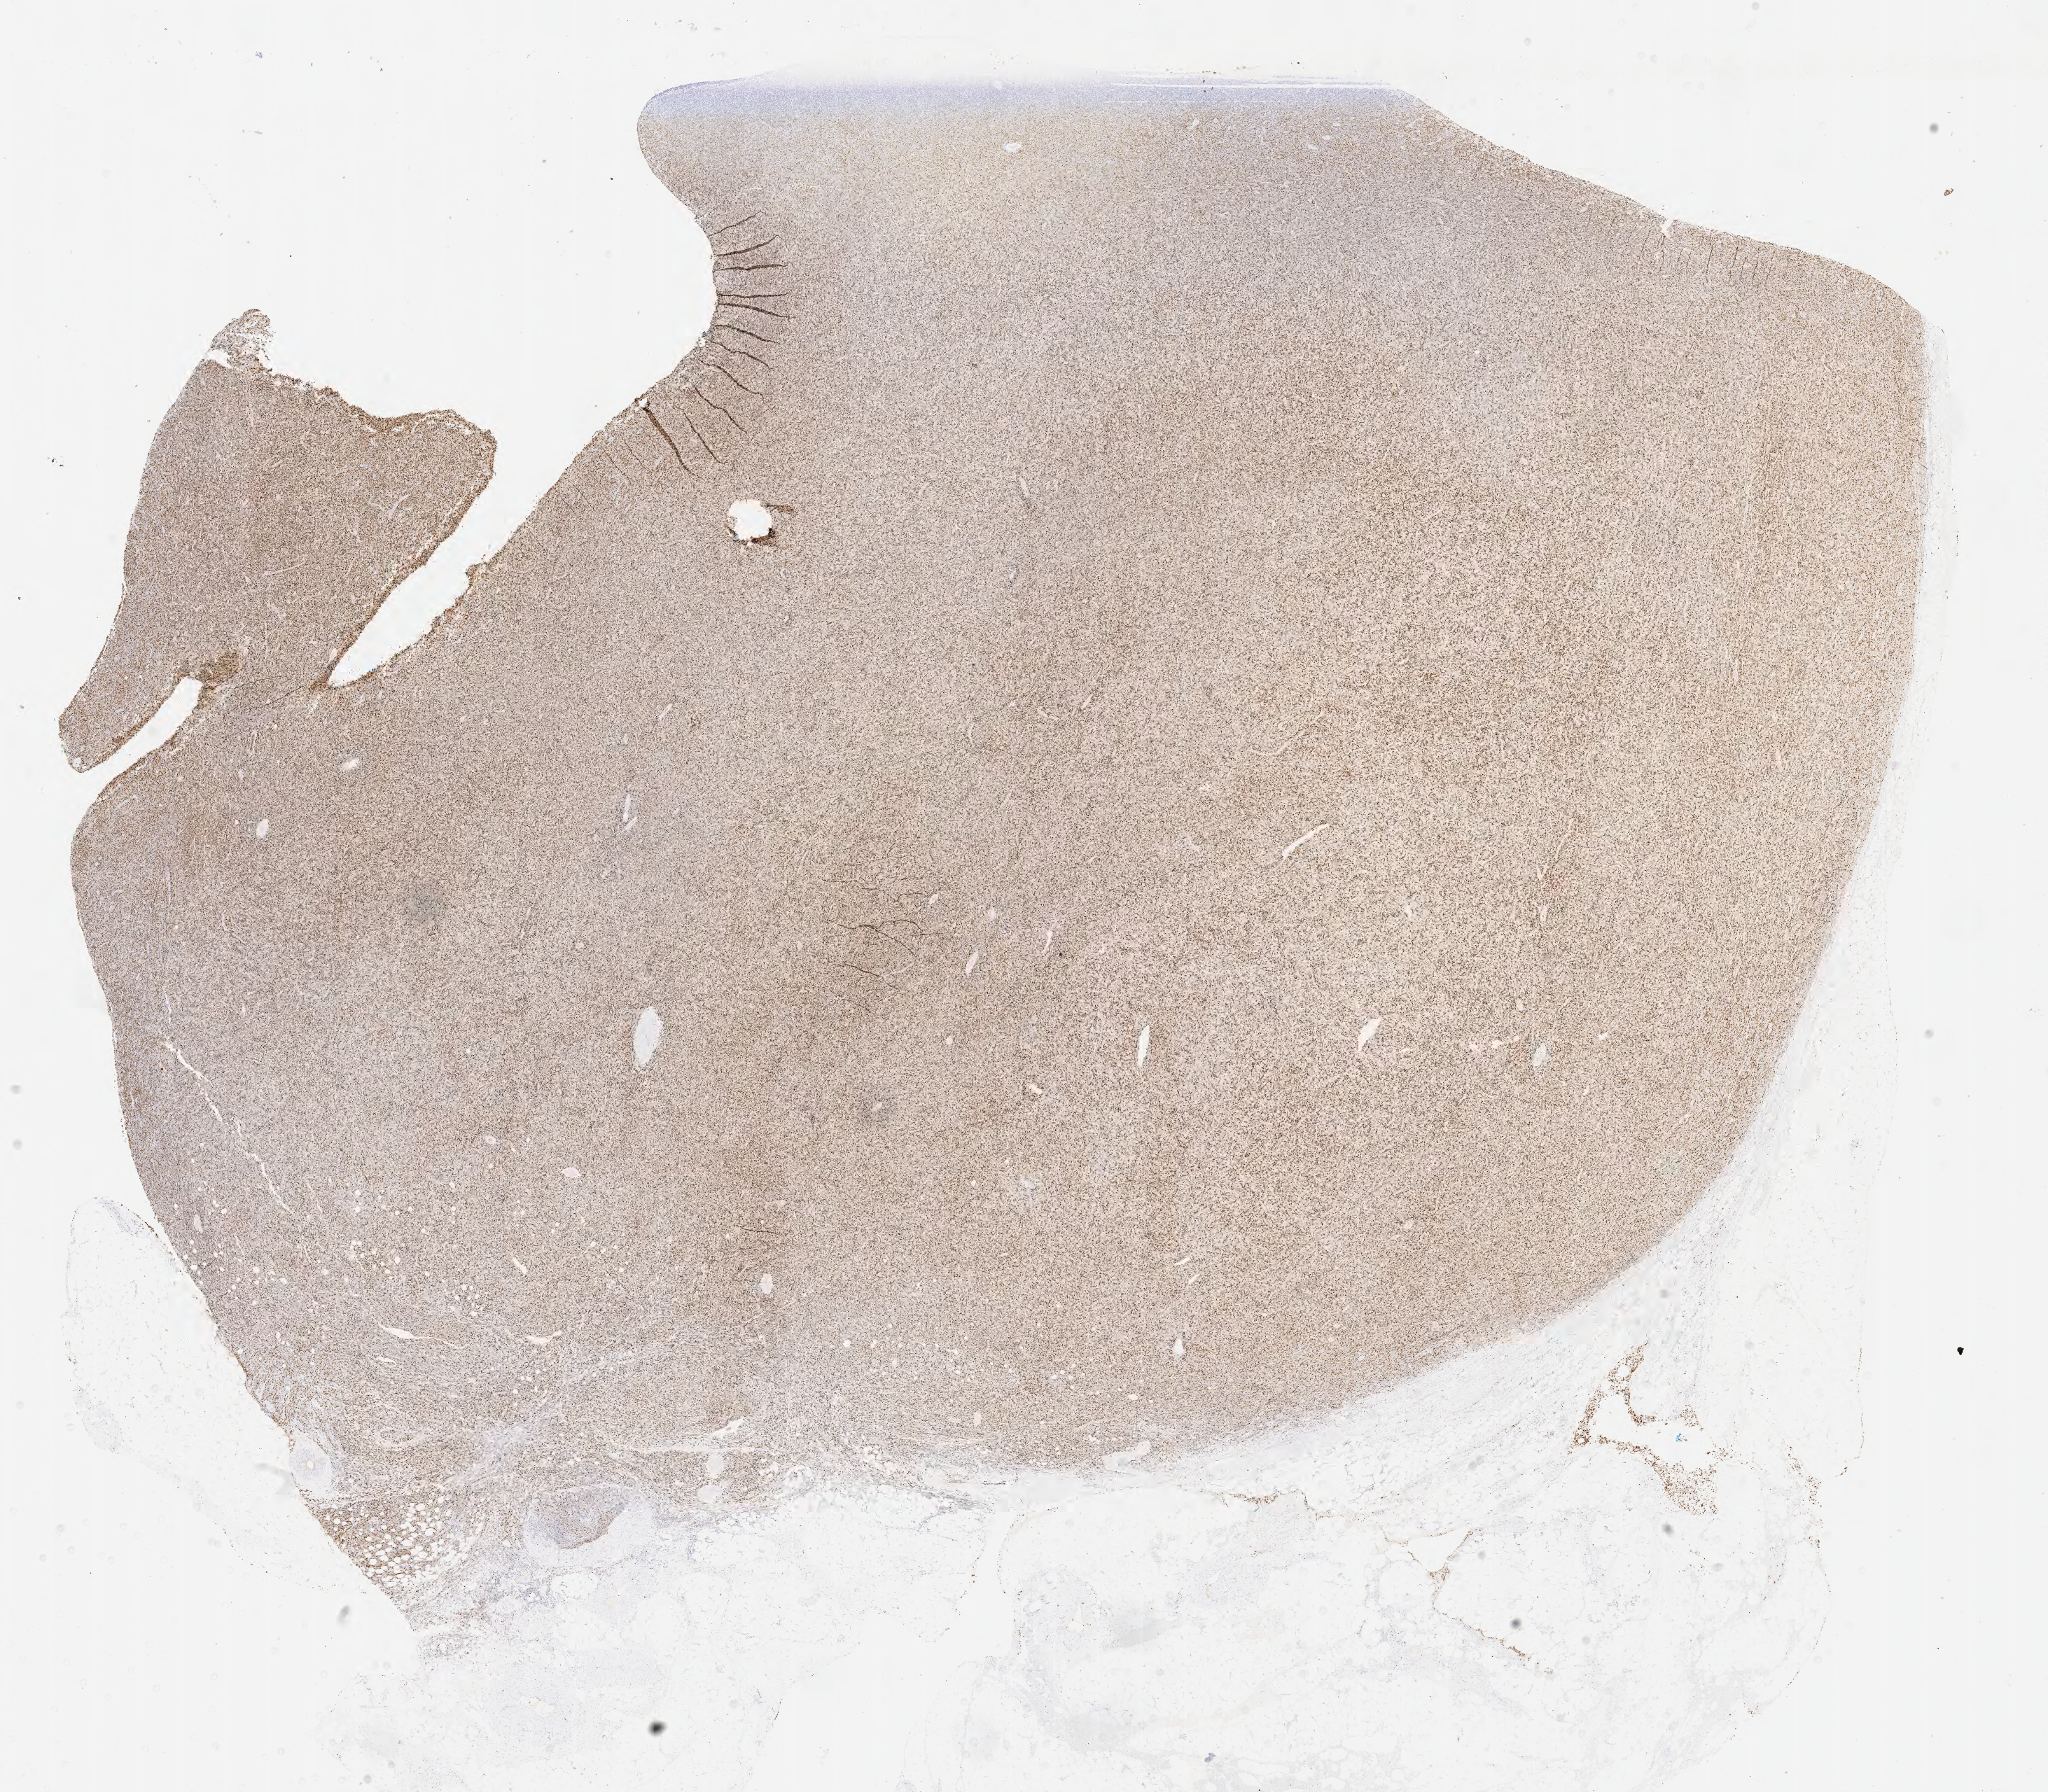
IHC for Ki-67, whole-slide image, shown as a low-resolution overview of the whole scanned area (about 23.6 x 20.7 mm), tumor tissue, site: lymph node. Patient: male, age 54 years.
Diagnosis: Diffuse large B-cell lymphoma, NOS.